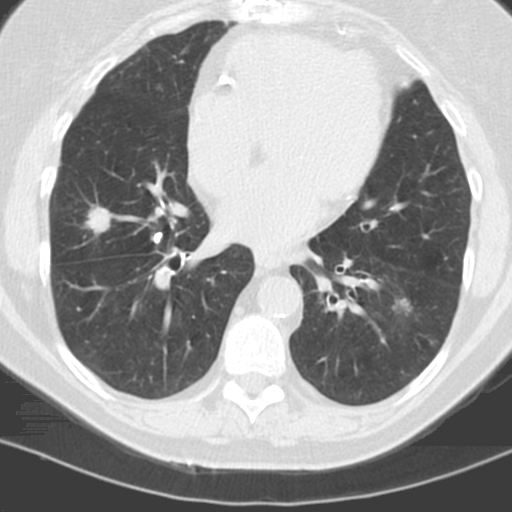
Low-dose screening chest CT, one axial slice; slice 47 of 121 in the series (ordered by position); 120 kVp; lung window (W 1500 / L -600 HU); 3.2 mm slice thickness; 512 × 512 image matrix, field of view 278 × 278 mm.
Structures marked on this image (expert manual segmentation):
- lesion 3 (tumor, middle lobe of right lung): box from (x=86, y=207) to (x=110, y=233) px